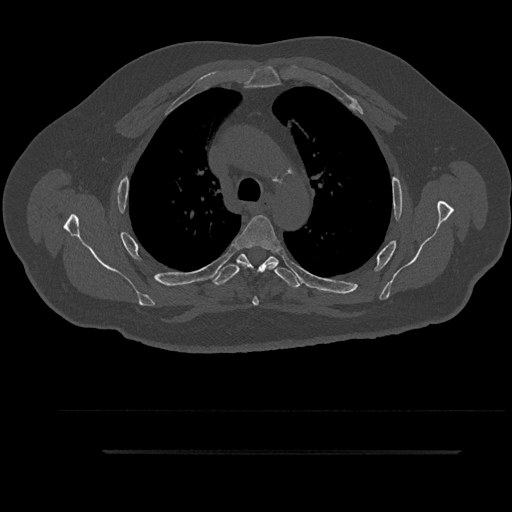
CT including the spine, one axial slice. Slice 653 of 797 in the series (ordered by position). Reconstruction kernel Br40s/3. 120 kVp. Bone window (W 1800 / L 400 HU). 512 × 512 image matrix. Male patient, age 63 years. Case-level facts recorded for this patient, not image findings: primary cancer: renal; vertebrae with lytic lesions (as recorded): T8.
Structures marked on this image (semi-automatic segmentation, software-assisted and operator-edited):
- T3 vertebra: bounding box <222,256,298,278> (left, top, right, bottom; pixels)
- T4 vertebra: <235,215,281,306>
- T5 vertebra: <213,254,300,289>